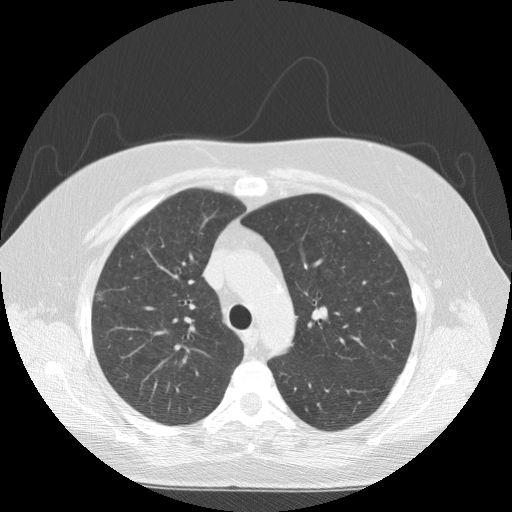
Axial slice from a low-dose chest CT screening exam. Baseline screening round. Lung window (W 1500 / L -600 HU). Standard (soft-tissue) reconstruction kernel (STANDARD). Slice 40 of 146 in the series. 512 × 512 image matrix, field of view 370 × 370 mm. Female participant, aged 55 years at enrolment. Current smoker at enrolment.
Expert reader's lesion annotation, bounding box [x1, y1, x2, y2] px = [78, 282, 121, 319]. The exam's reader record, not a measurement of the box and not confirmed to be the same lesion: non-calcified nodule or mass ≥4 mm, right upper lobe, 8 × 7 mm, spiculated (stellate) margins, soft tissue attenuation. Lung cancer was diagnosed 98 days after this screen: squamous cell carcinoma, NOS, right upper lobe, poorly differentiated (G3), stage IA (AJCC 6th edition), 8 mm at pathology.